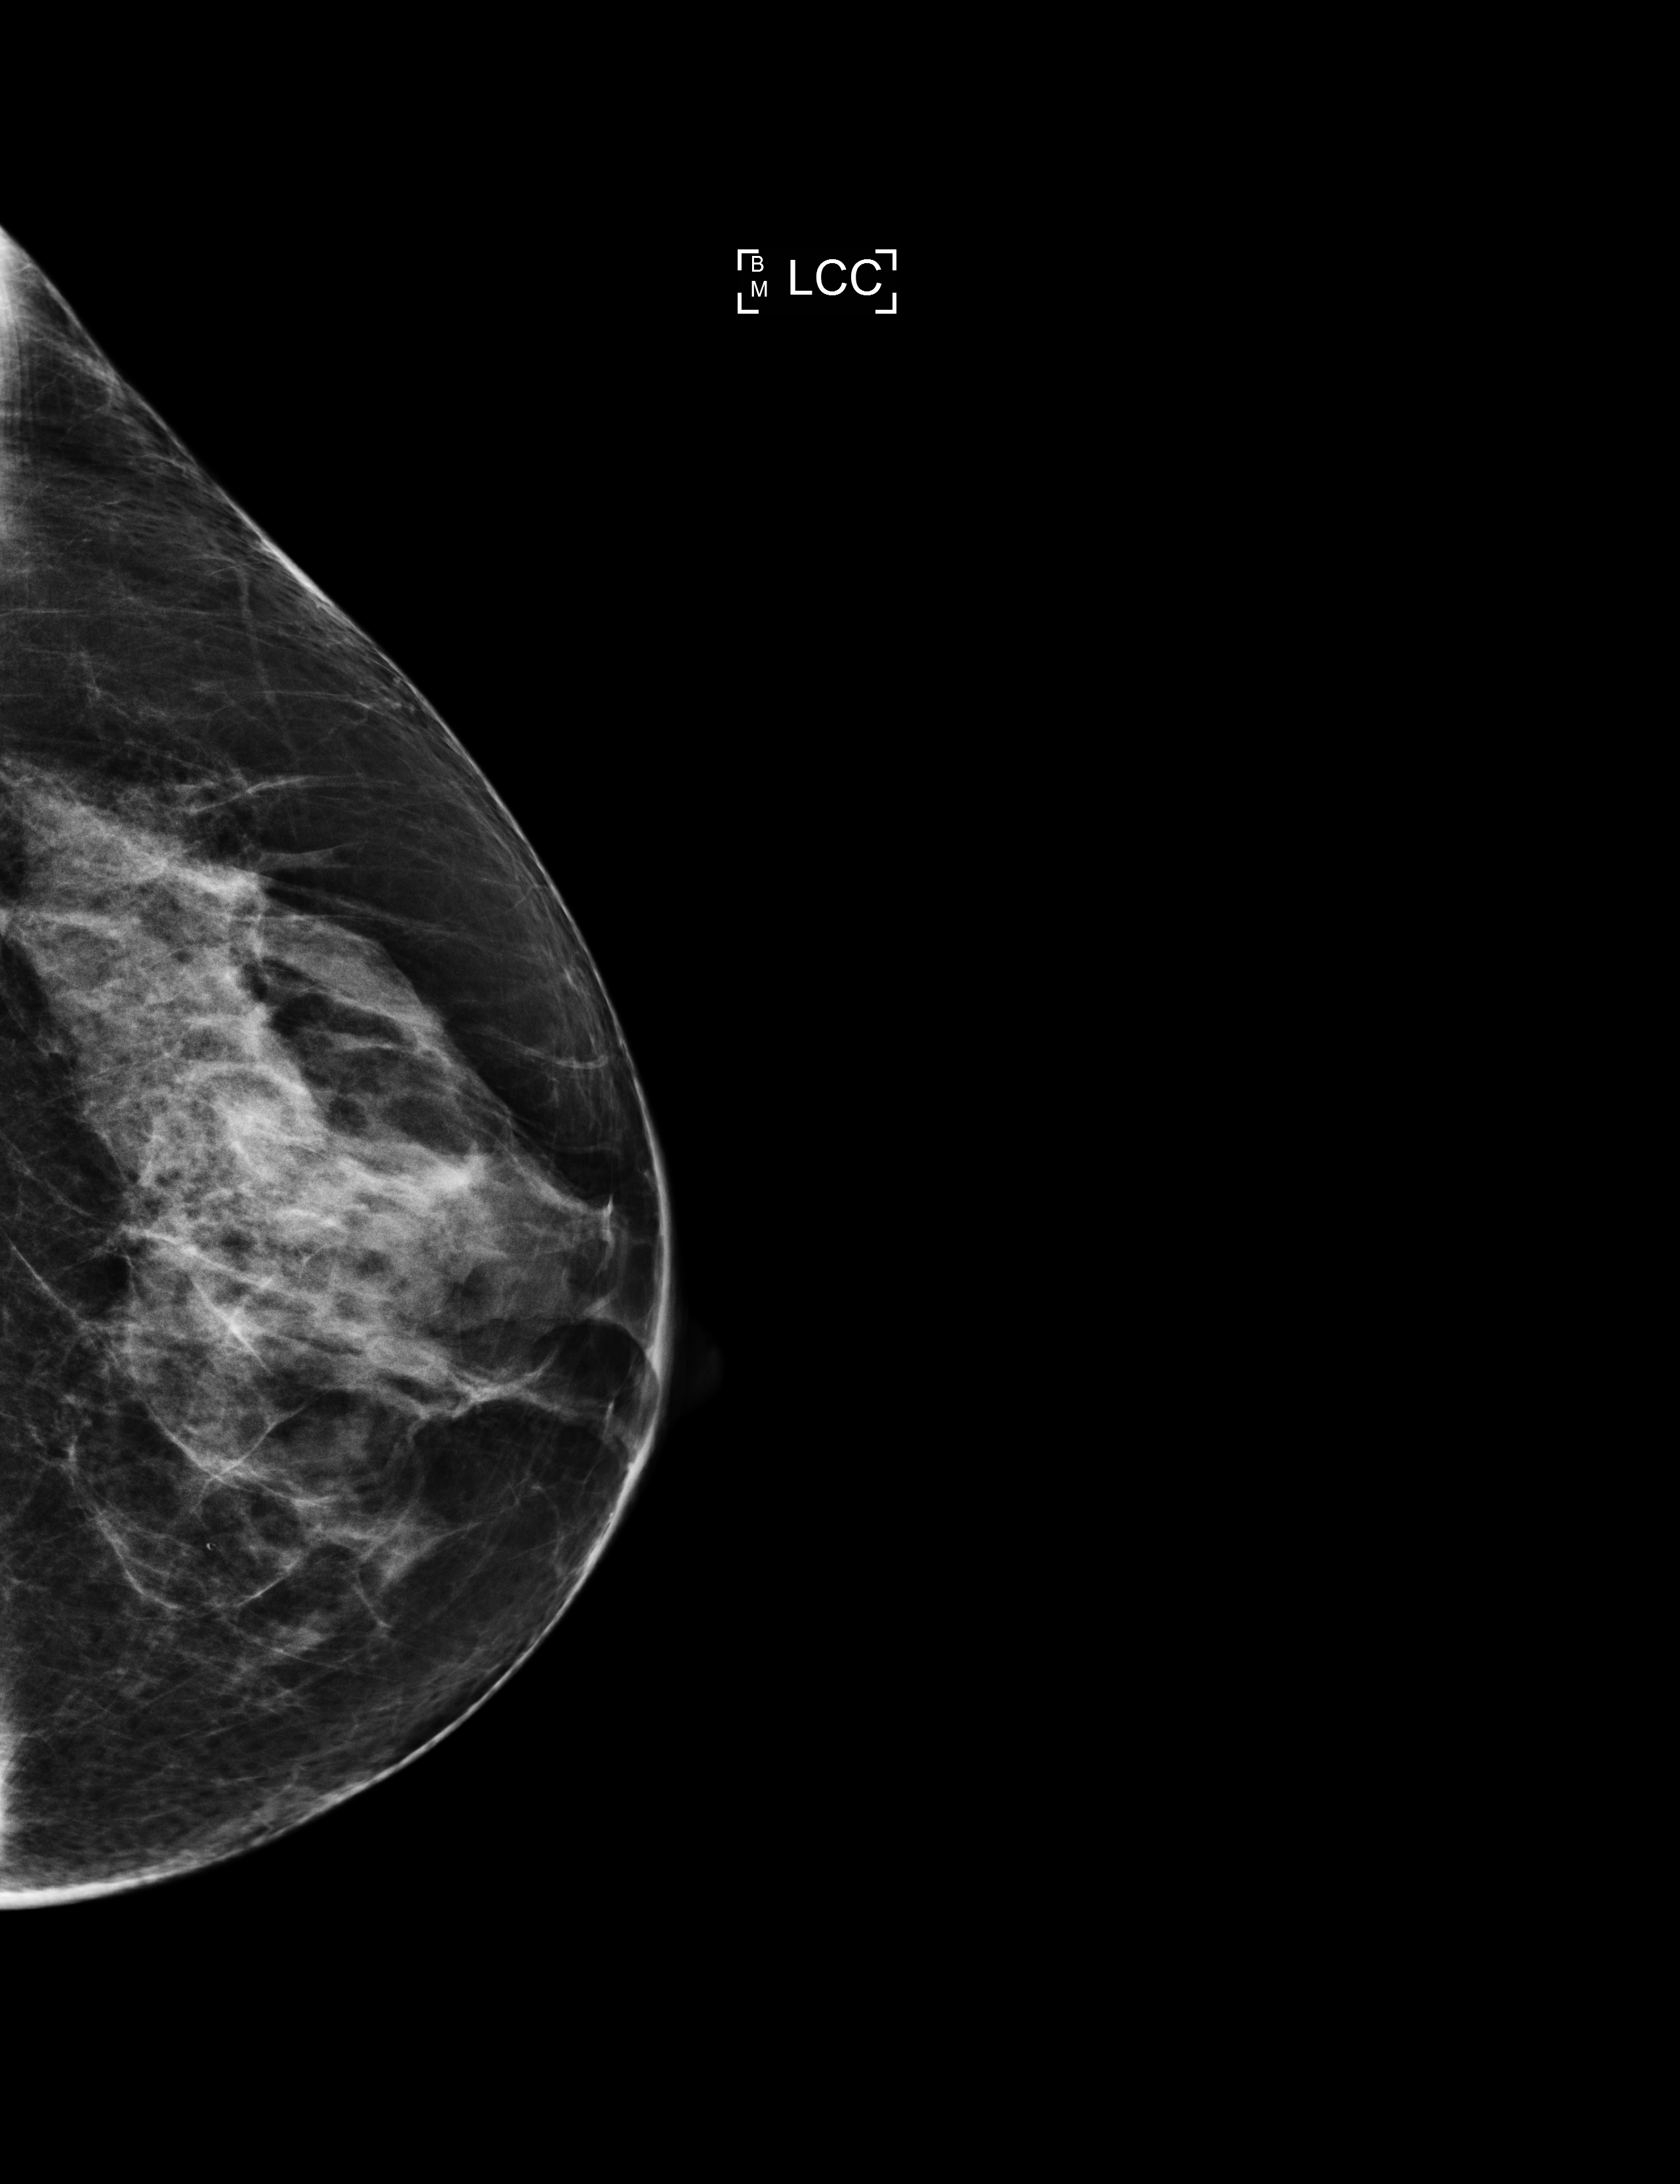
Annual screening mammography examination. Female patient, age 60 years.
Image type: full-field digital mammogram. Breast: left. Projection: CC view.